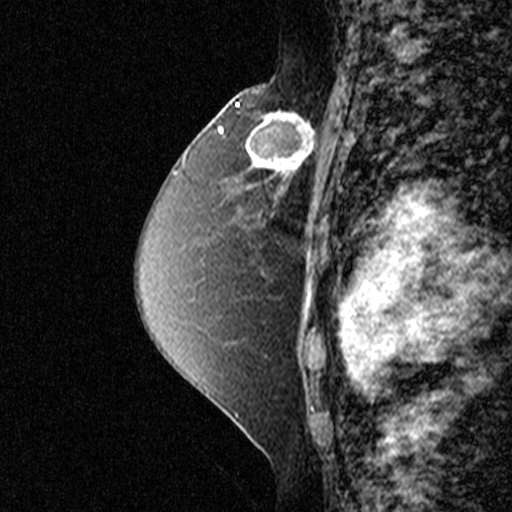
Breast MRI (dynamic contrast-enhanced), one sagittal slice. Position 27 of 44 along the scan axis. Dynamic contrast-enhanced study with each time point stored as its own series, time point 2 of 3 at this slice position (early post-contrast, ordered by acquisition time). 1.5 T. TE 4.5 ms, TR 11 ms. 3 mm slice thickness. 512 × 512 image matrix. Patient: female, 49 years. Case-level facts recorded for this patient, not image findings: setting: breast cancer imaged before/during neoadjuvant chemotherapy; receptor status: triple-negative.
Outlined on this slice (semi-automatic segmentation, software-assisted and operator-edited):
- analysis volume of interest (the breast-tissue region the enhancement analysis was run in; not a lesion): box from (x=244, y=100) to (x=335, y=197) px
- tumour enhancement mask (voxels above the 90 % enhancement threshold inside the analysis volume of interest): (x=252, y=111)–(x=314, y=197)